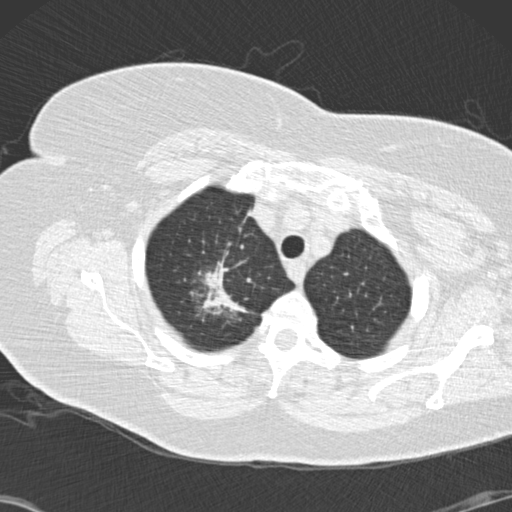
Low-dose screening chest CT, one axial slice. Position 123 of 146 along the scan axis. Lung window (W 1500 / L -600 HU). 512 × 512 image matrix, field of view 350 × 350 mm.
Structures marked on this image (manually delineated by an expert):
- lesion 1 (tumor, upper lobe of right lung): box from (x=203, y=261) to (x=247, y=315) px